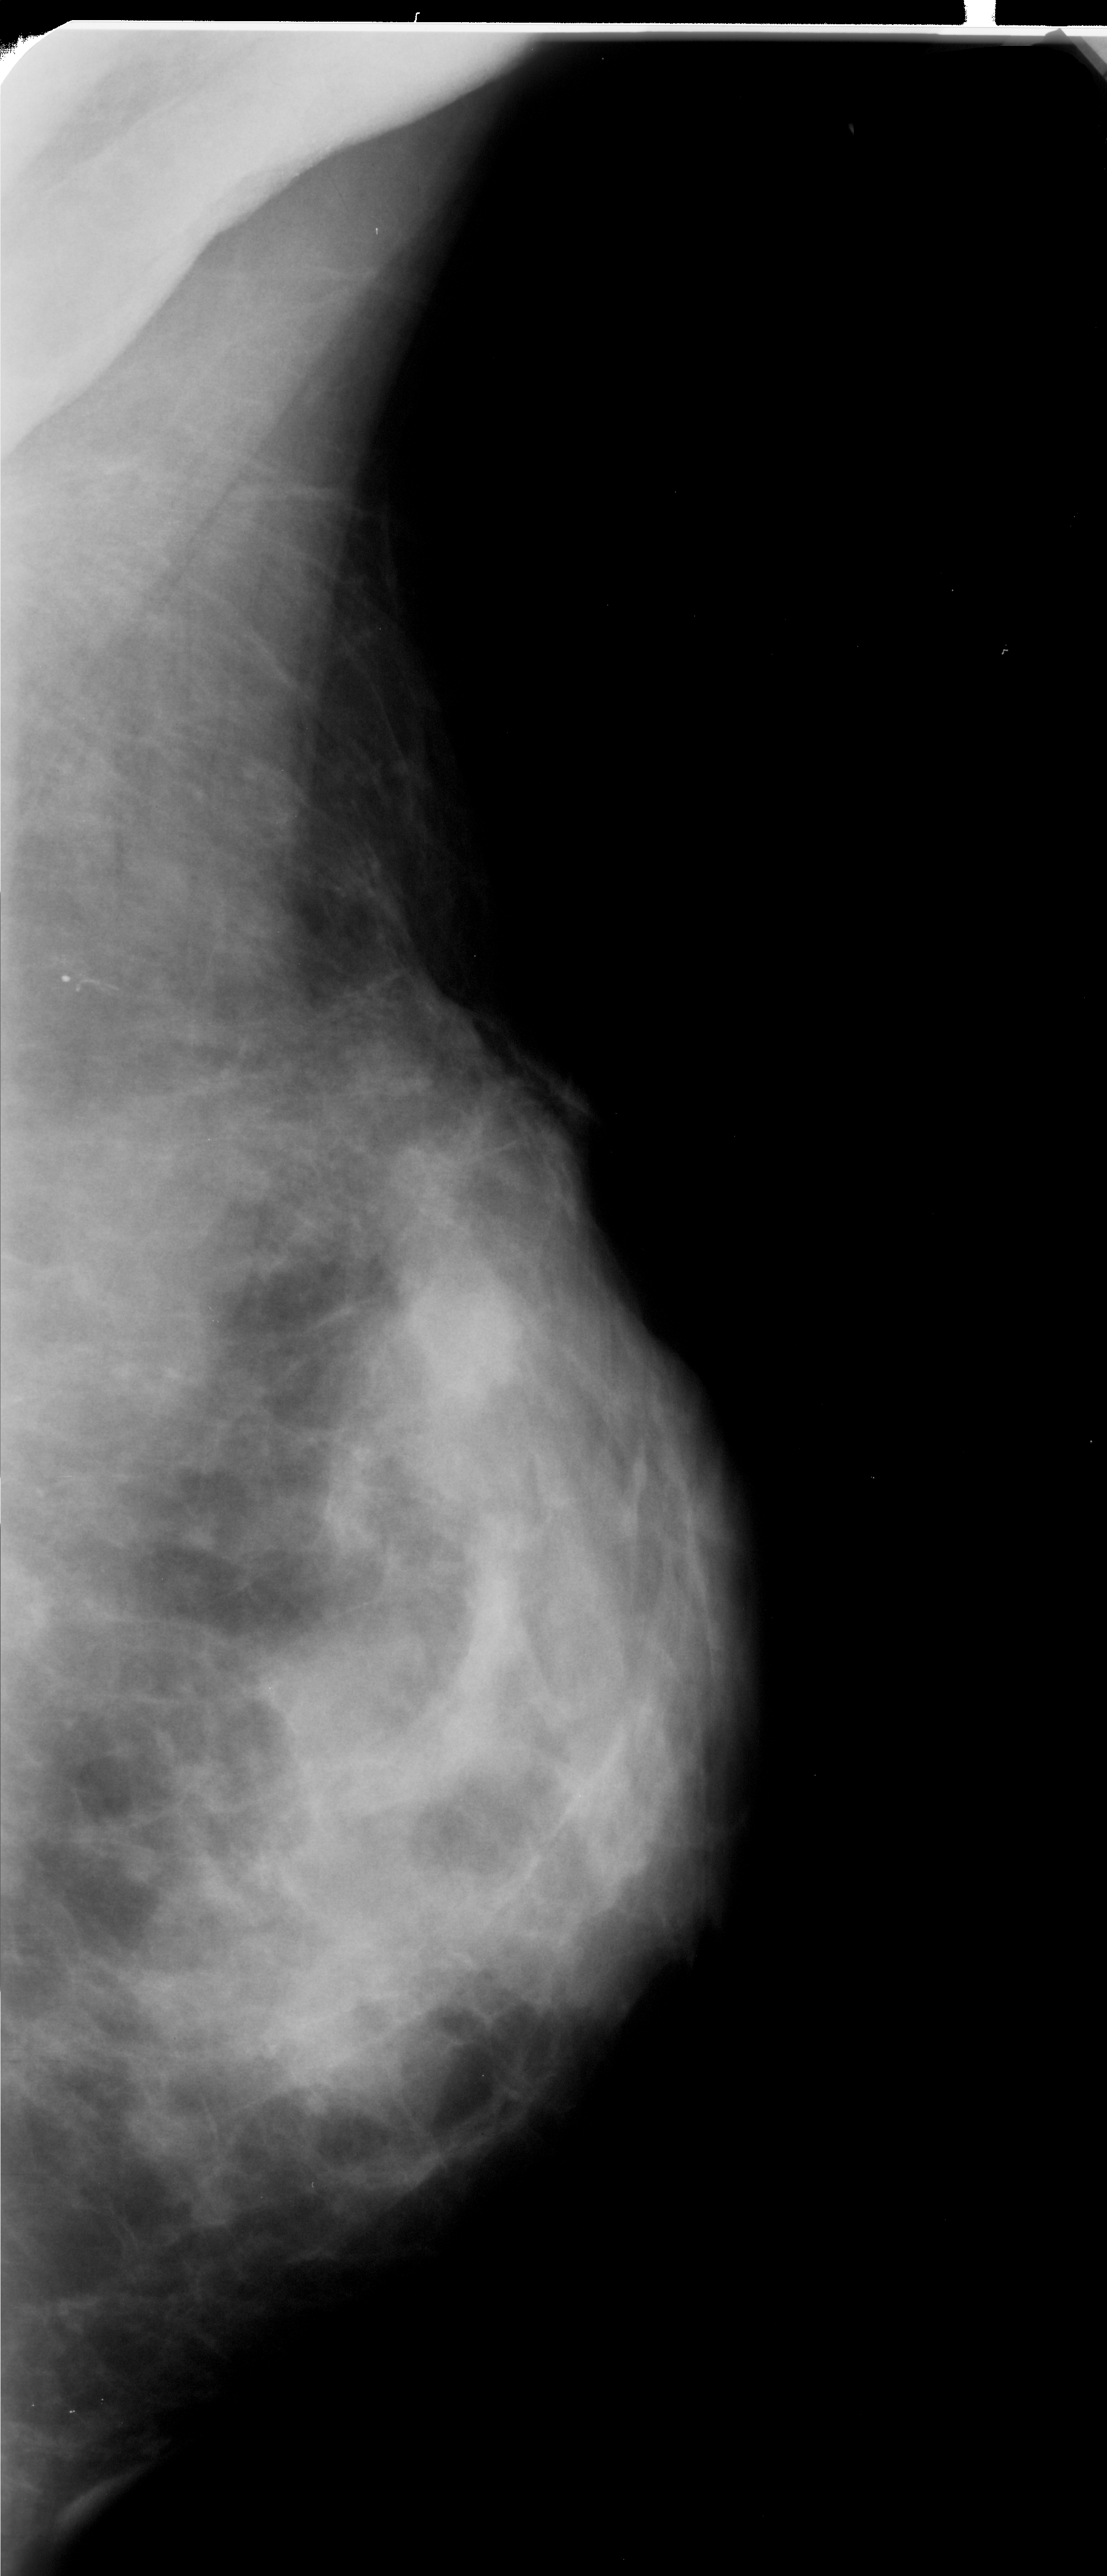
Mammogram (digitized film); right breast; mediolateral oblique (MLO) view; breast composition: extremely dense (BI-RADS density category 4 of 4).
Marked findings (only marked abnormalities are described; nothing is implied about the rest of the image): calcifications, morphology fine linear branching, distribution linear; BI-RADS assessment category 4; pathology (as recorded): malignant.